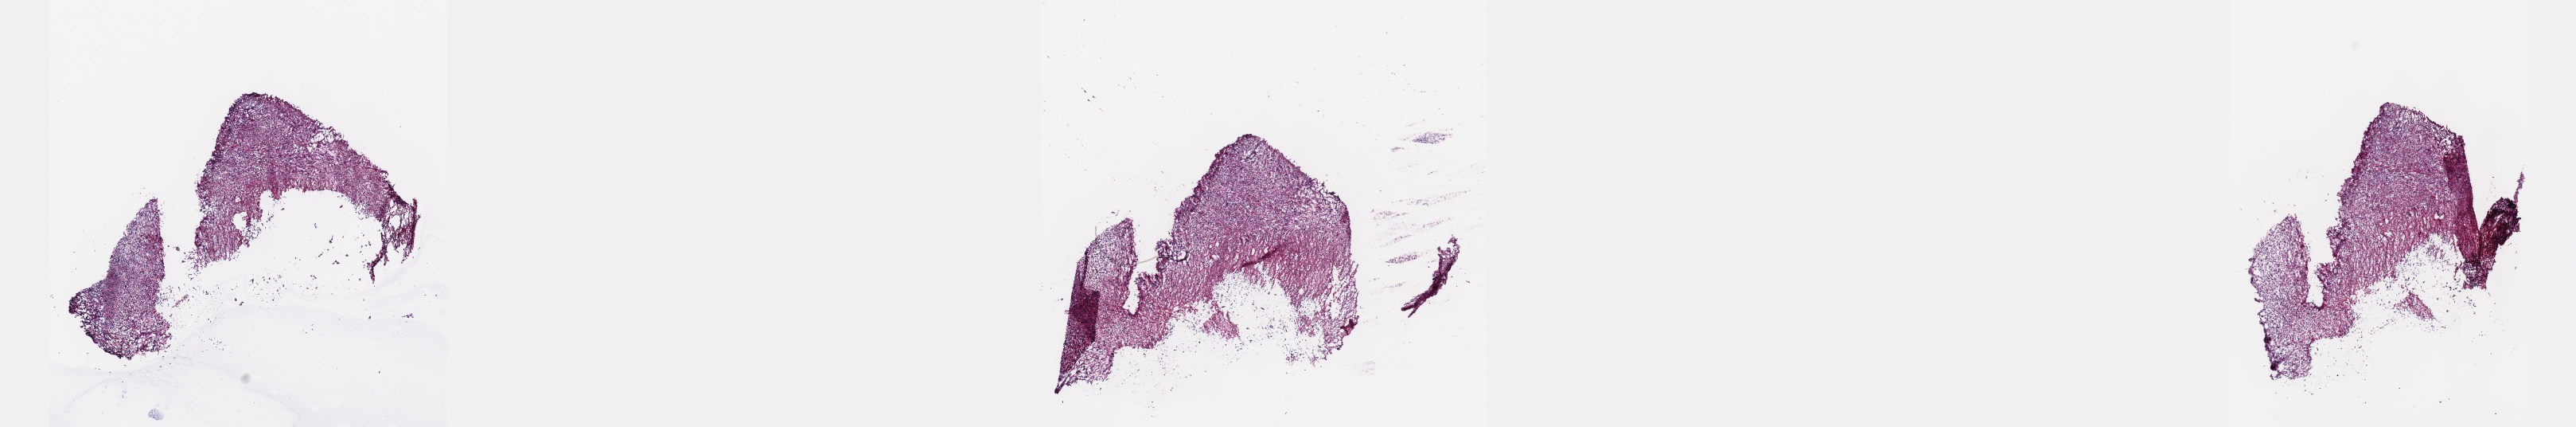
Digitized Hematoxylin and eosin (H&E) stained tissue section (whole slide), whole scanned area (about 26.2 x 4.3 mm, slide scanned at 40x) shown as a low-resolution overview; frozen section from the top of the tissue portion; sample: primary tumour, connective, subcutaneous and other soft tissues. Male patient. Pathologist review of this section (percent, as recorded): tumour cells 100%, tumour nuclei 80%, normal cells 0%, stromal cells 0%, necrosis 0%. Infiltration values recorded for this section: lymphocyte infiltration 1%, monocyte infiltration 0%, neutrophil infiltration 0%.
• histologic diagnosis: Fibromyxosarcoma (connective, subcutaneous and other soft tissues of lower limb and hip)